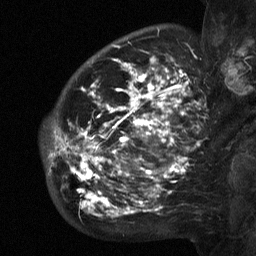
Breast MRI (dynamic contrast-enhanced), one sagittal slice. Slice 44 of 64 in the series (ordered by position). Dynamic contrast-enhanced study with each time point stored as its own series, time point 2 of 3 at this slice position (early post-contrast, ordered by acquisition time). 1.5 T. TE 4.8 ms, TR 27 ms. 256 × 256 image matrix, field of view 200 × 200 mm. Female patient, age 50 years. From the clinical record (not read from this slice): setting: breast cancer imaged before/during neoadjuvant chemotherapy; receptor status: HER2-positive.
Annotated regions visible in this slice (semi-automatically segmented with operator editing):
- analysis volume of interest (the breast-tissue region the enhancement analysis was run in; not a lesion): bounding box [x1, y1, x2, y2] px = [53, 64, 208, 218]
- tumour enhancement mask (voxels above the 90 % enhancement threshold inside the analysis volume of interest): [53, 64, 200, 216]